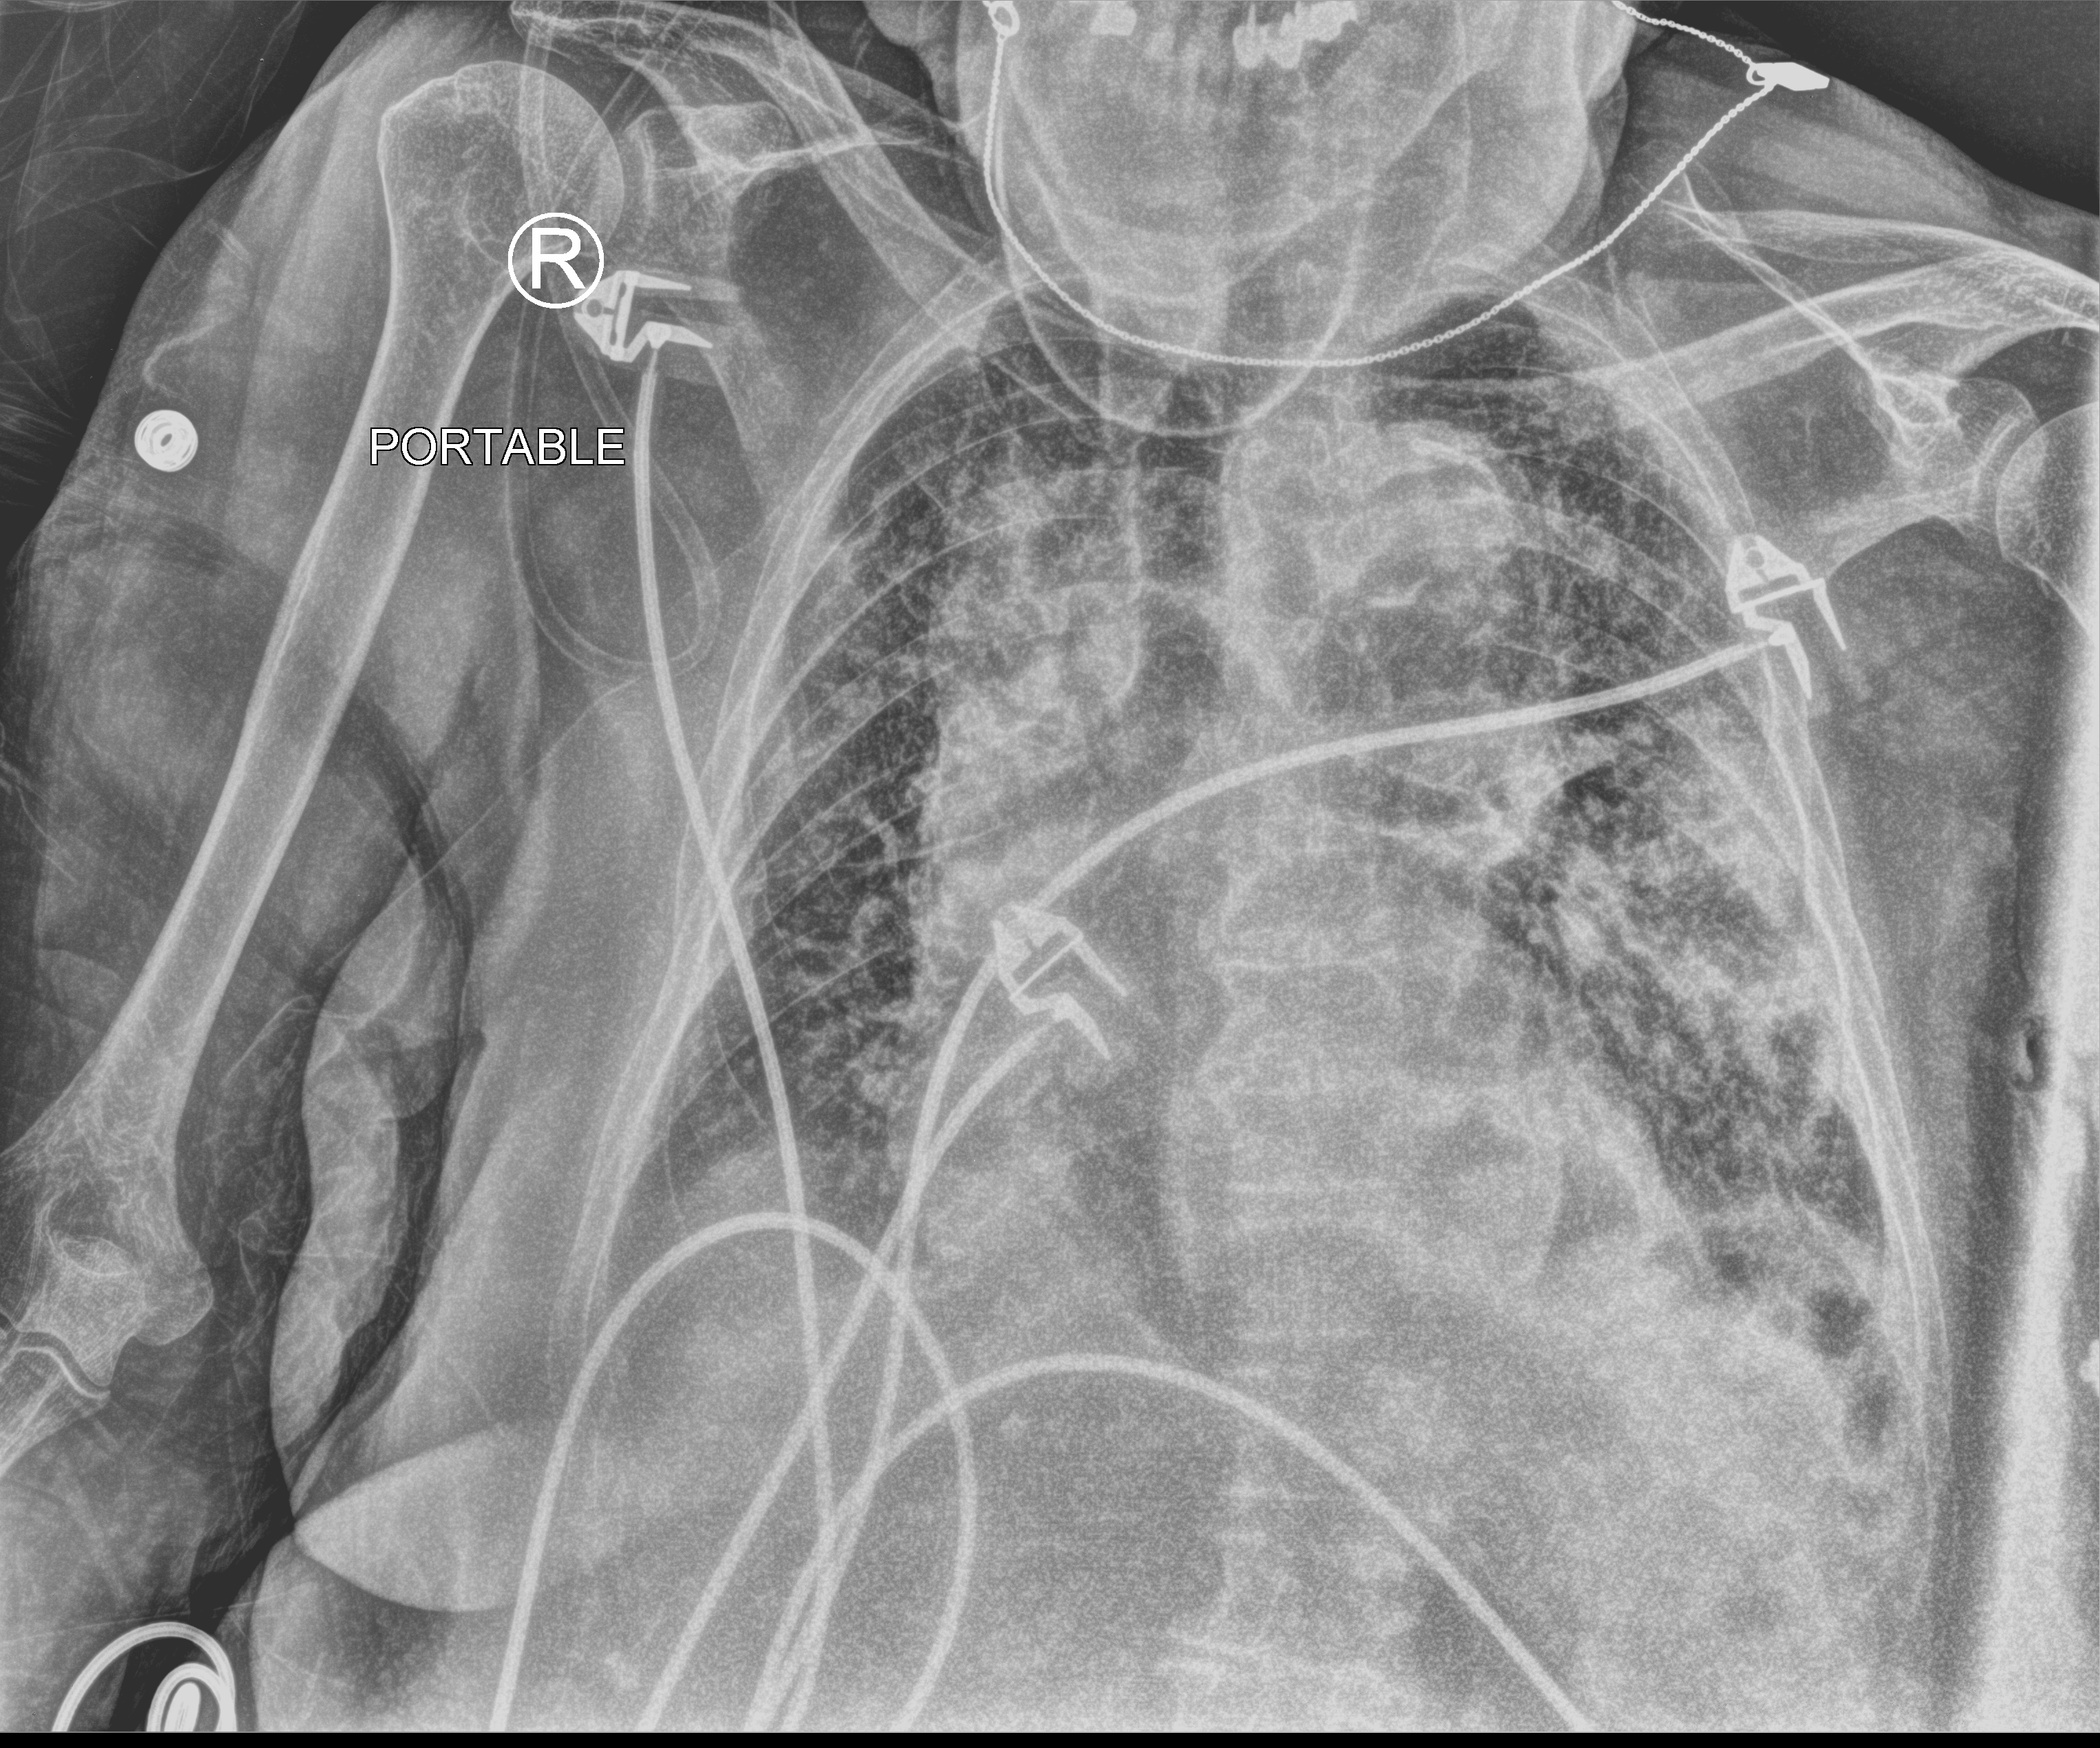
Portable chest radiograph. Patient hospitalised with COVID-19; female, aged 75–90 years.
From the hospital-stay record, not from the radiograph (when in the stay this image was taken is not recorded):
- admitted to intensive care during this hospital stay: no